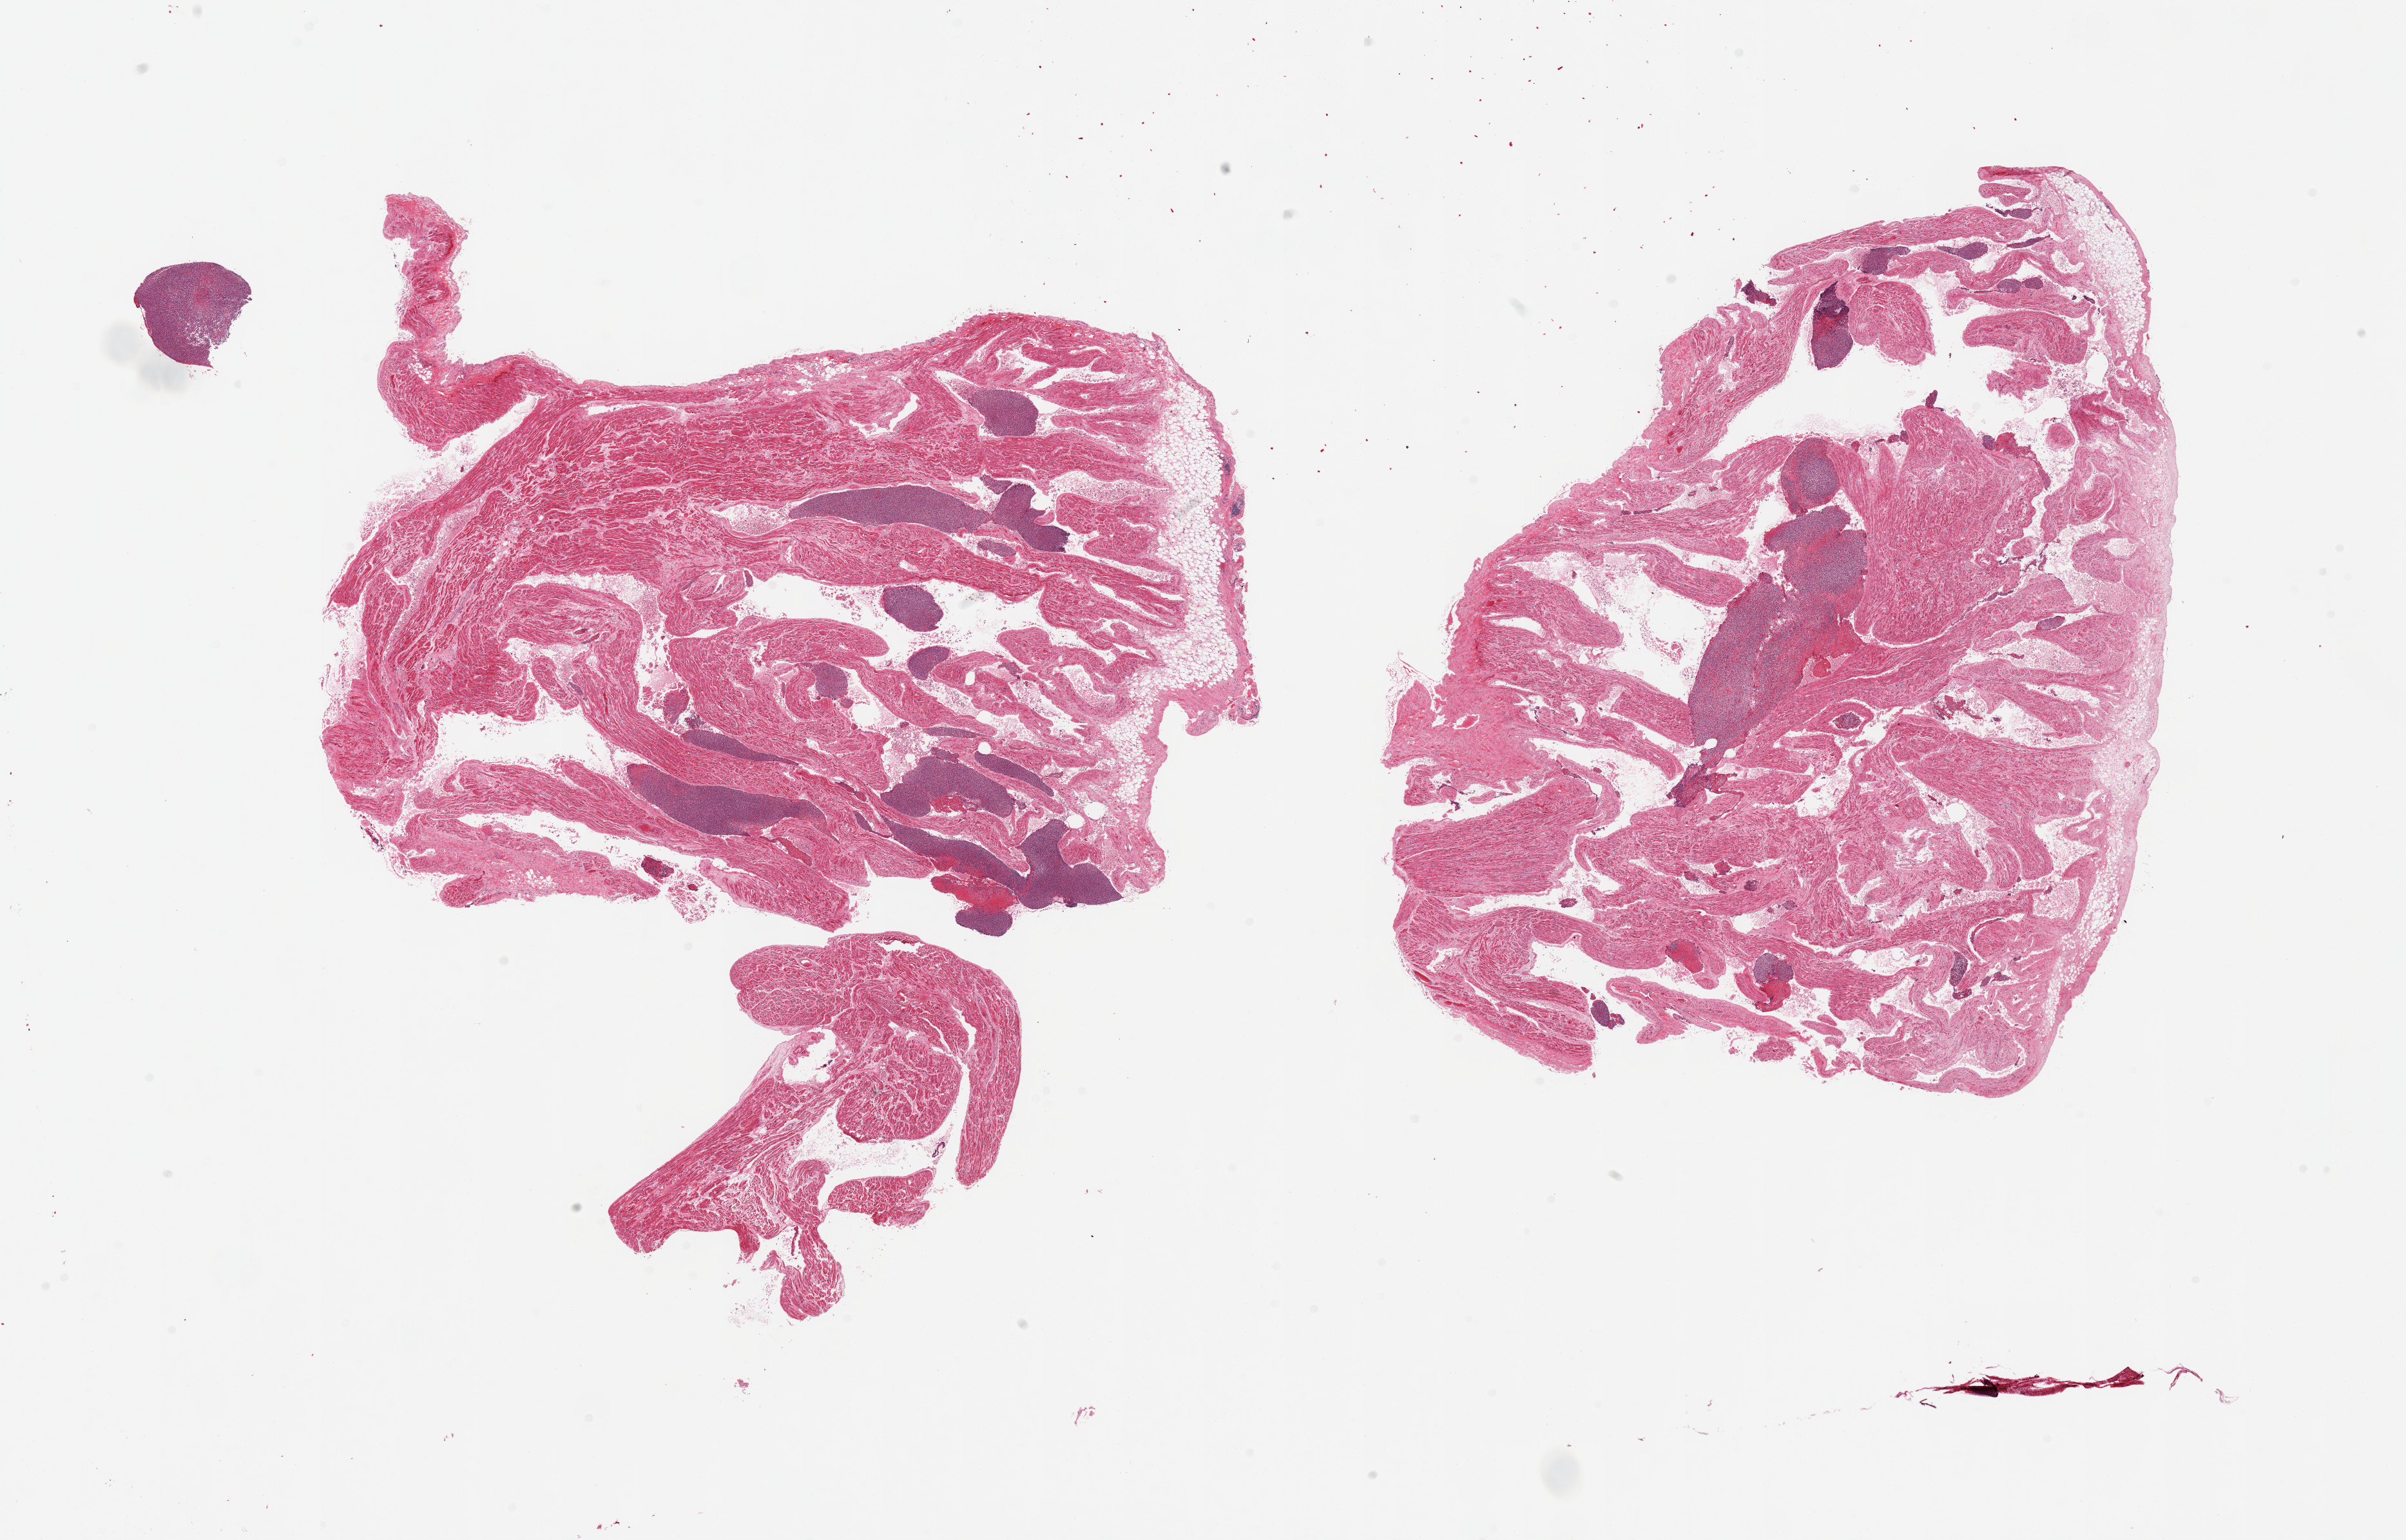
H&E whole-slide image — shown as a low-resolution overview of the whole scanned area (about 29.5 x 18.9 mm); PAXgene-fixed paraffin-embedded (PFPE) section; sampled site (target tissue): auricular appendage; donor tissue sample. Male donor.
- review note (as recorded): 2 pieces, mulitple acute inflammatory aggregates/miscroabscesses